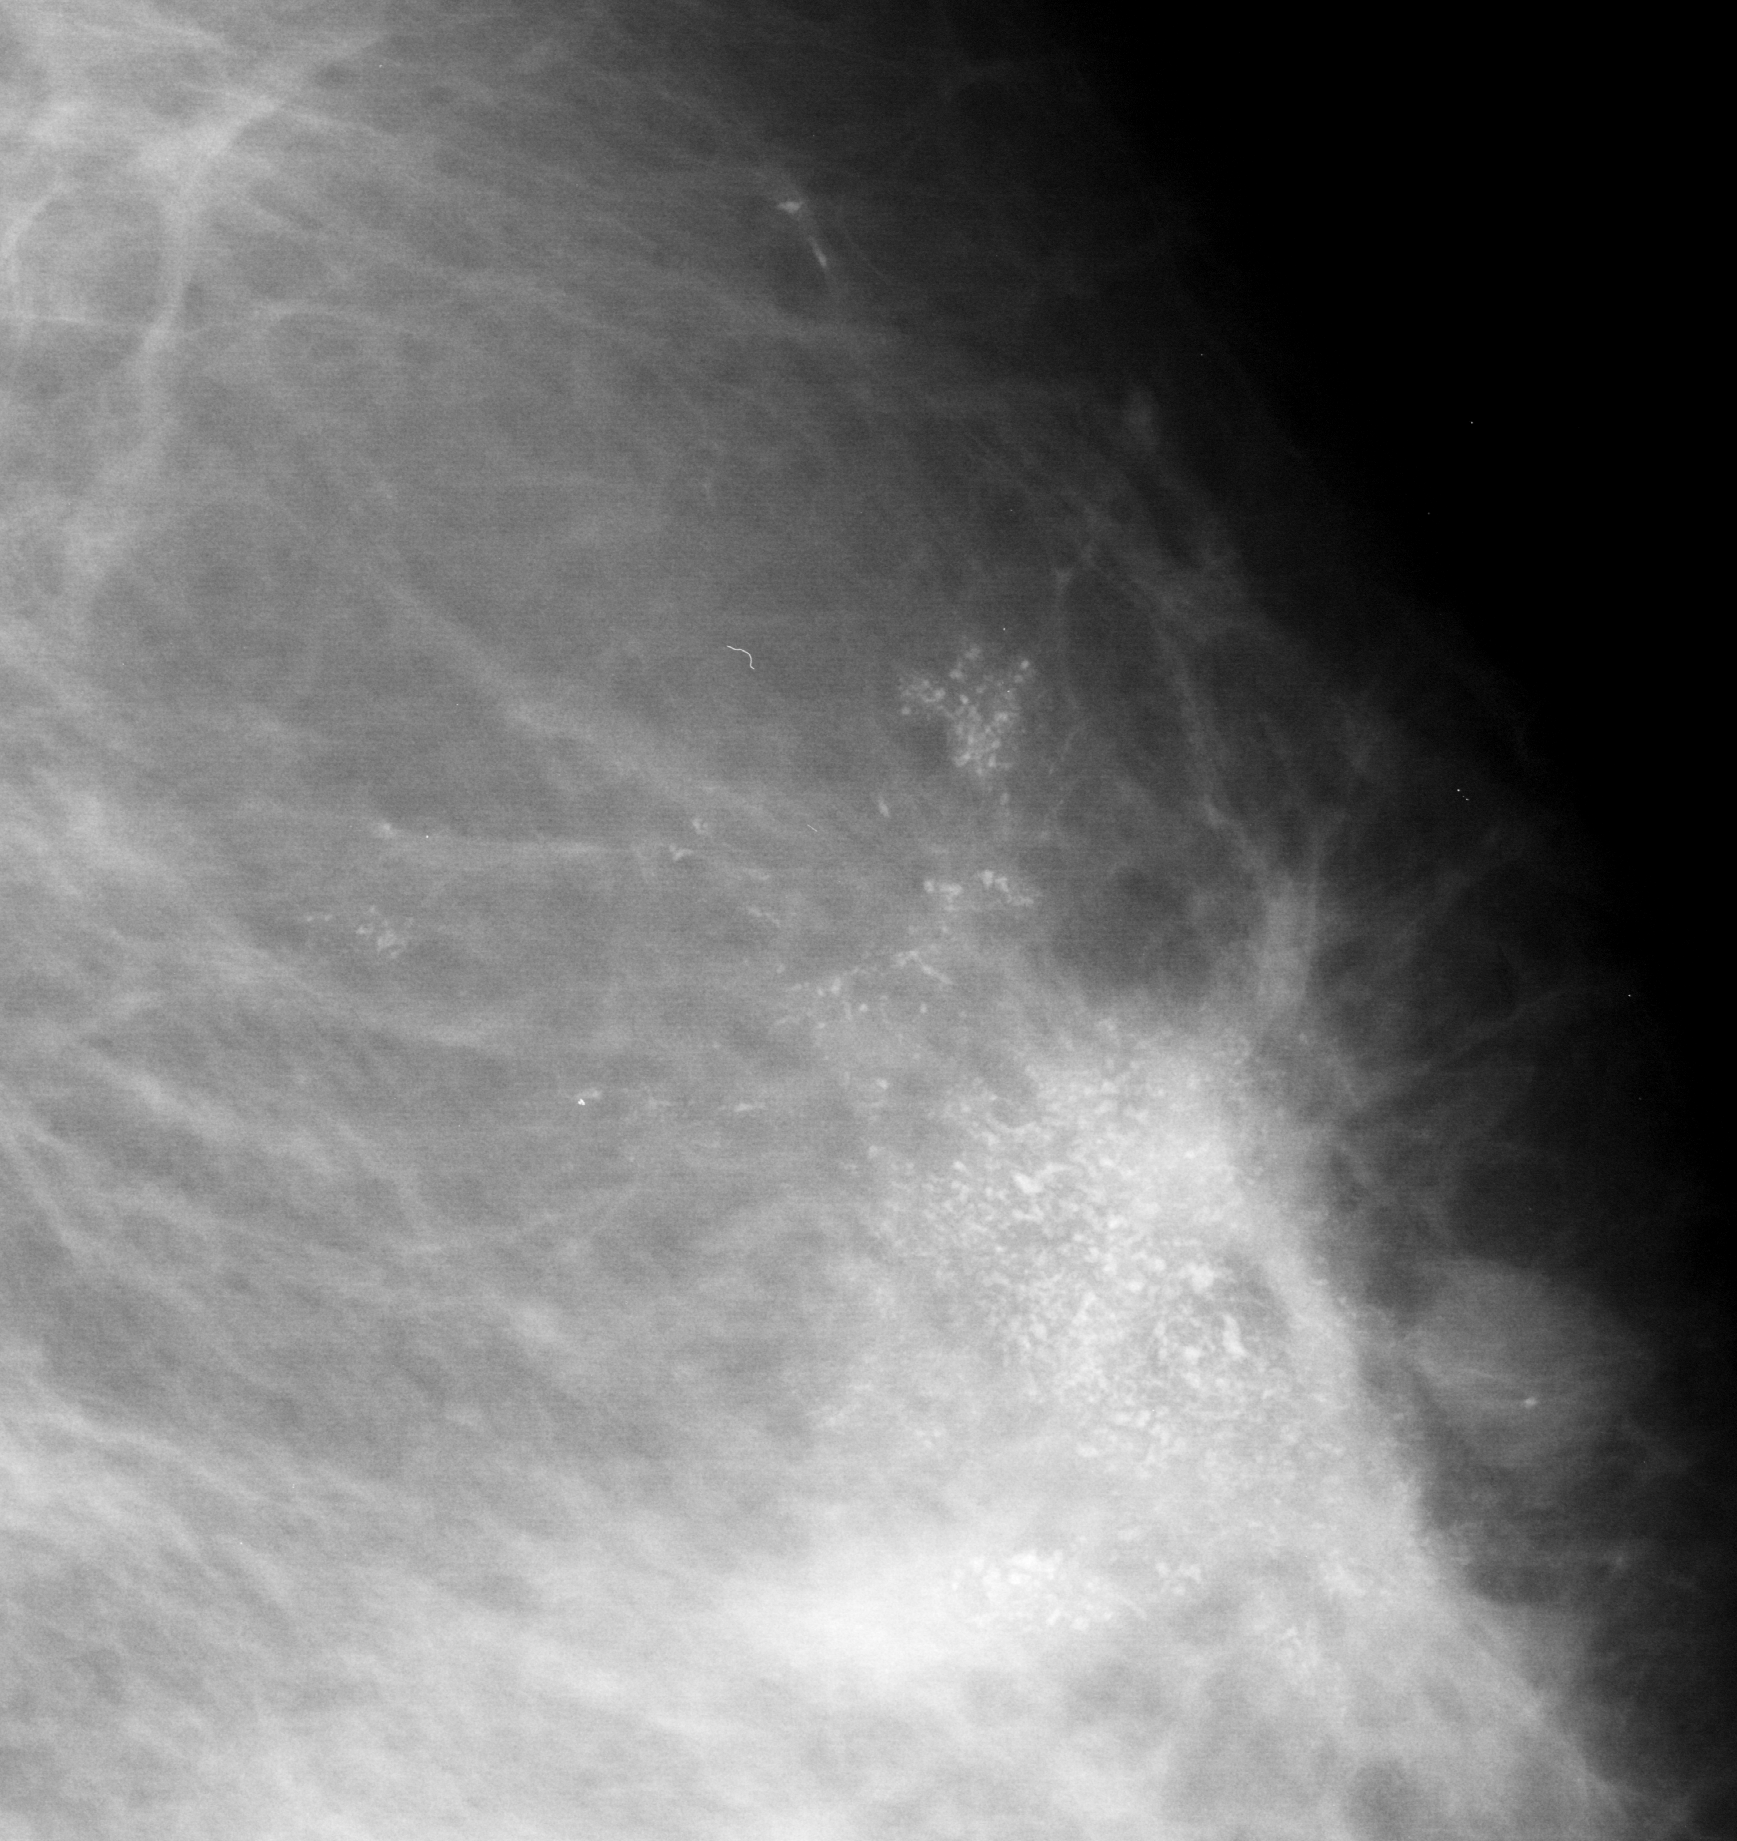
Cropped region of a digitized screen-film mammogram centred on a radiologist-marked abnormality; left breast; MLO view.
Marked abnormality: calcifications, morphology pleomorphic, distribution segmental; BI-RADS assessment category 5; subtlety rating 5 on a 1 (subtle) to 5 (obvious) scale; pathology result (as recorded, not read from the image): malignant.